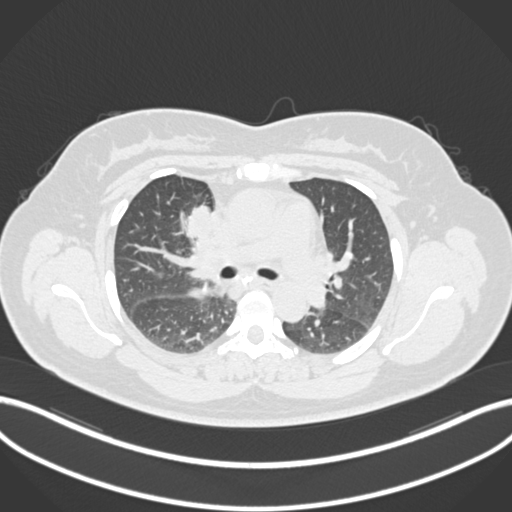
Chest CT, one axial slice. Position 110 of 183 along the scan axis. Reconstruction kernel B30f. Lung window (W 1500 / L -600 HU). 1 mm slice thickness. 512 × 512 image matrix. Patient: female, 46 years. Case-level facts recorded for this patient, not image findings: clinical TNM (as recorded): T2a N1 M0.
Annotated regions visible in this slice (rectangle marked by the reading radiologist):
- lung tumour (recorded histology: adenocarcinoma): box from (x=184, y=203) to (x=216, y=246) px